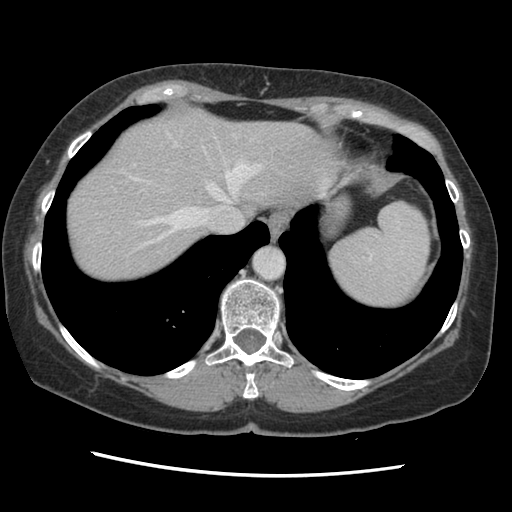
Contrast-enhanced abdominal CT, one axial slice; slice 116 of 141 in the series (ordered by position); soft-tissue window (W 400 / L 40 HU); 512 × 512 image matrix. Female patient, age 61 years. Case-level facts recorded for this patient, not image findings: diagnosis: colorectal cancer liver metastases, imaged before liver resection; multiple liver metastases: no; largest metastasis: 2.4 cm; chemotherapy before resection: no.
Outlined on this slice (expert manual segmentation):
- hepatic veins: bounding box [x1, y1, x2, y2] px = [134, 132, 261, 250]
- liver: [66, 108, 337, 283]
- planned liver remnant (the part of the liver to remain after resection): [66, 107, 337, 283]